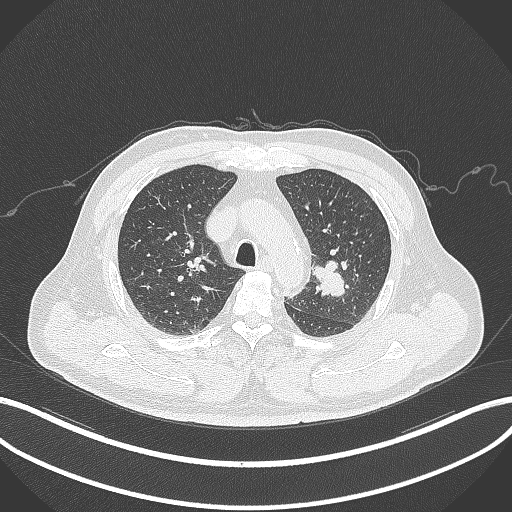
Chest CT, one axial slice. Slice 226 of 286 in the series (ordered by position). 120 kVp. Lung window (W 1500 / L -600 HU). 512 × 512 image matrix, field of view 400 × 400 mm. Male patient, age 67 years. Case-level facts recorded for this patient, not image findings: clinical TNM (as recorded): T2a N1 M0; histopathological grade: G3.
Annotated regions visible in this slice (bounding box drawn by a radiologist):
- lung tumour (recorded histology: adenocarcinoma): bounding box [x1, y1, x2, y2] px = [310, 256, 348, 299]